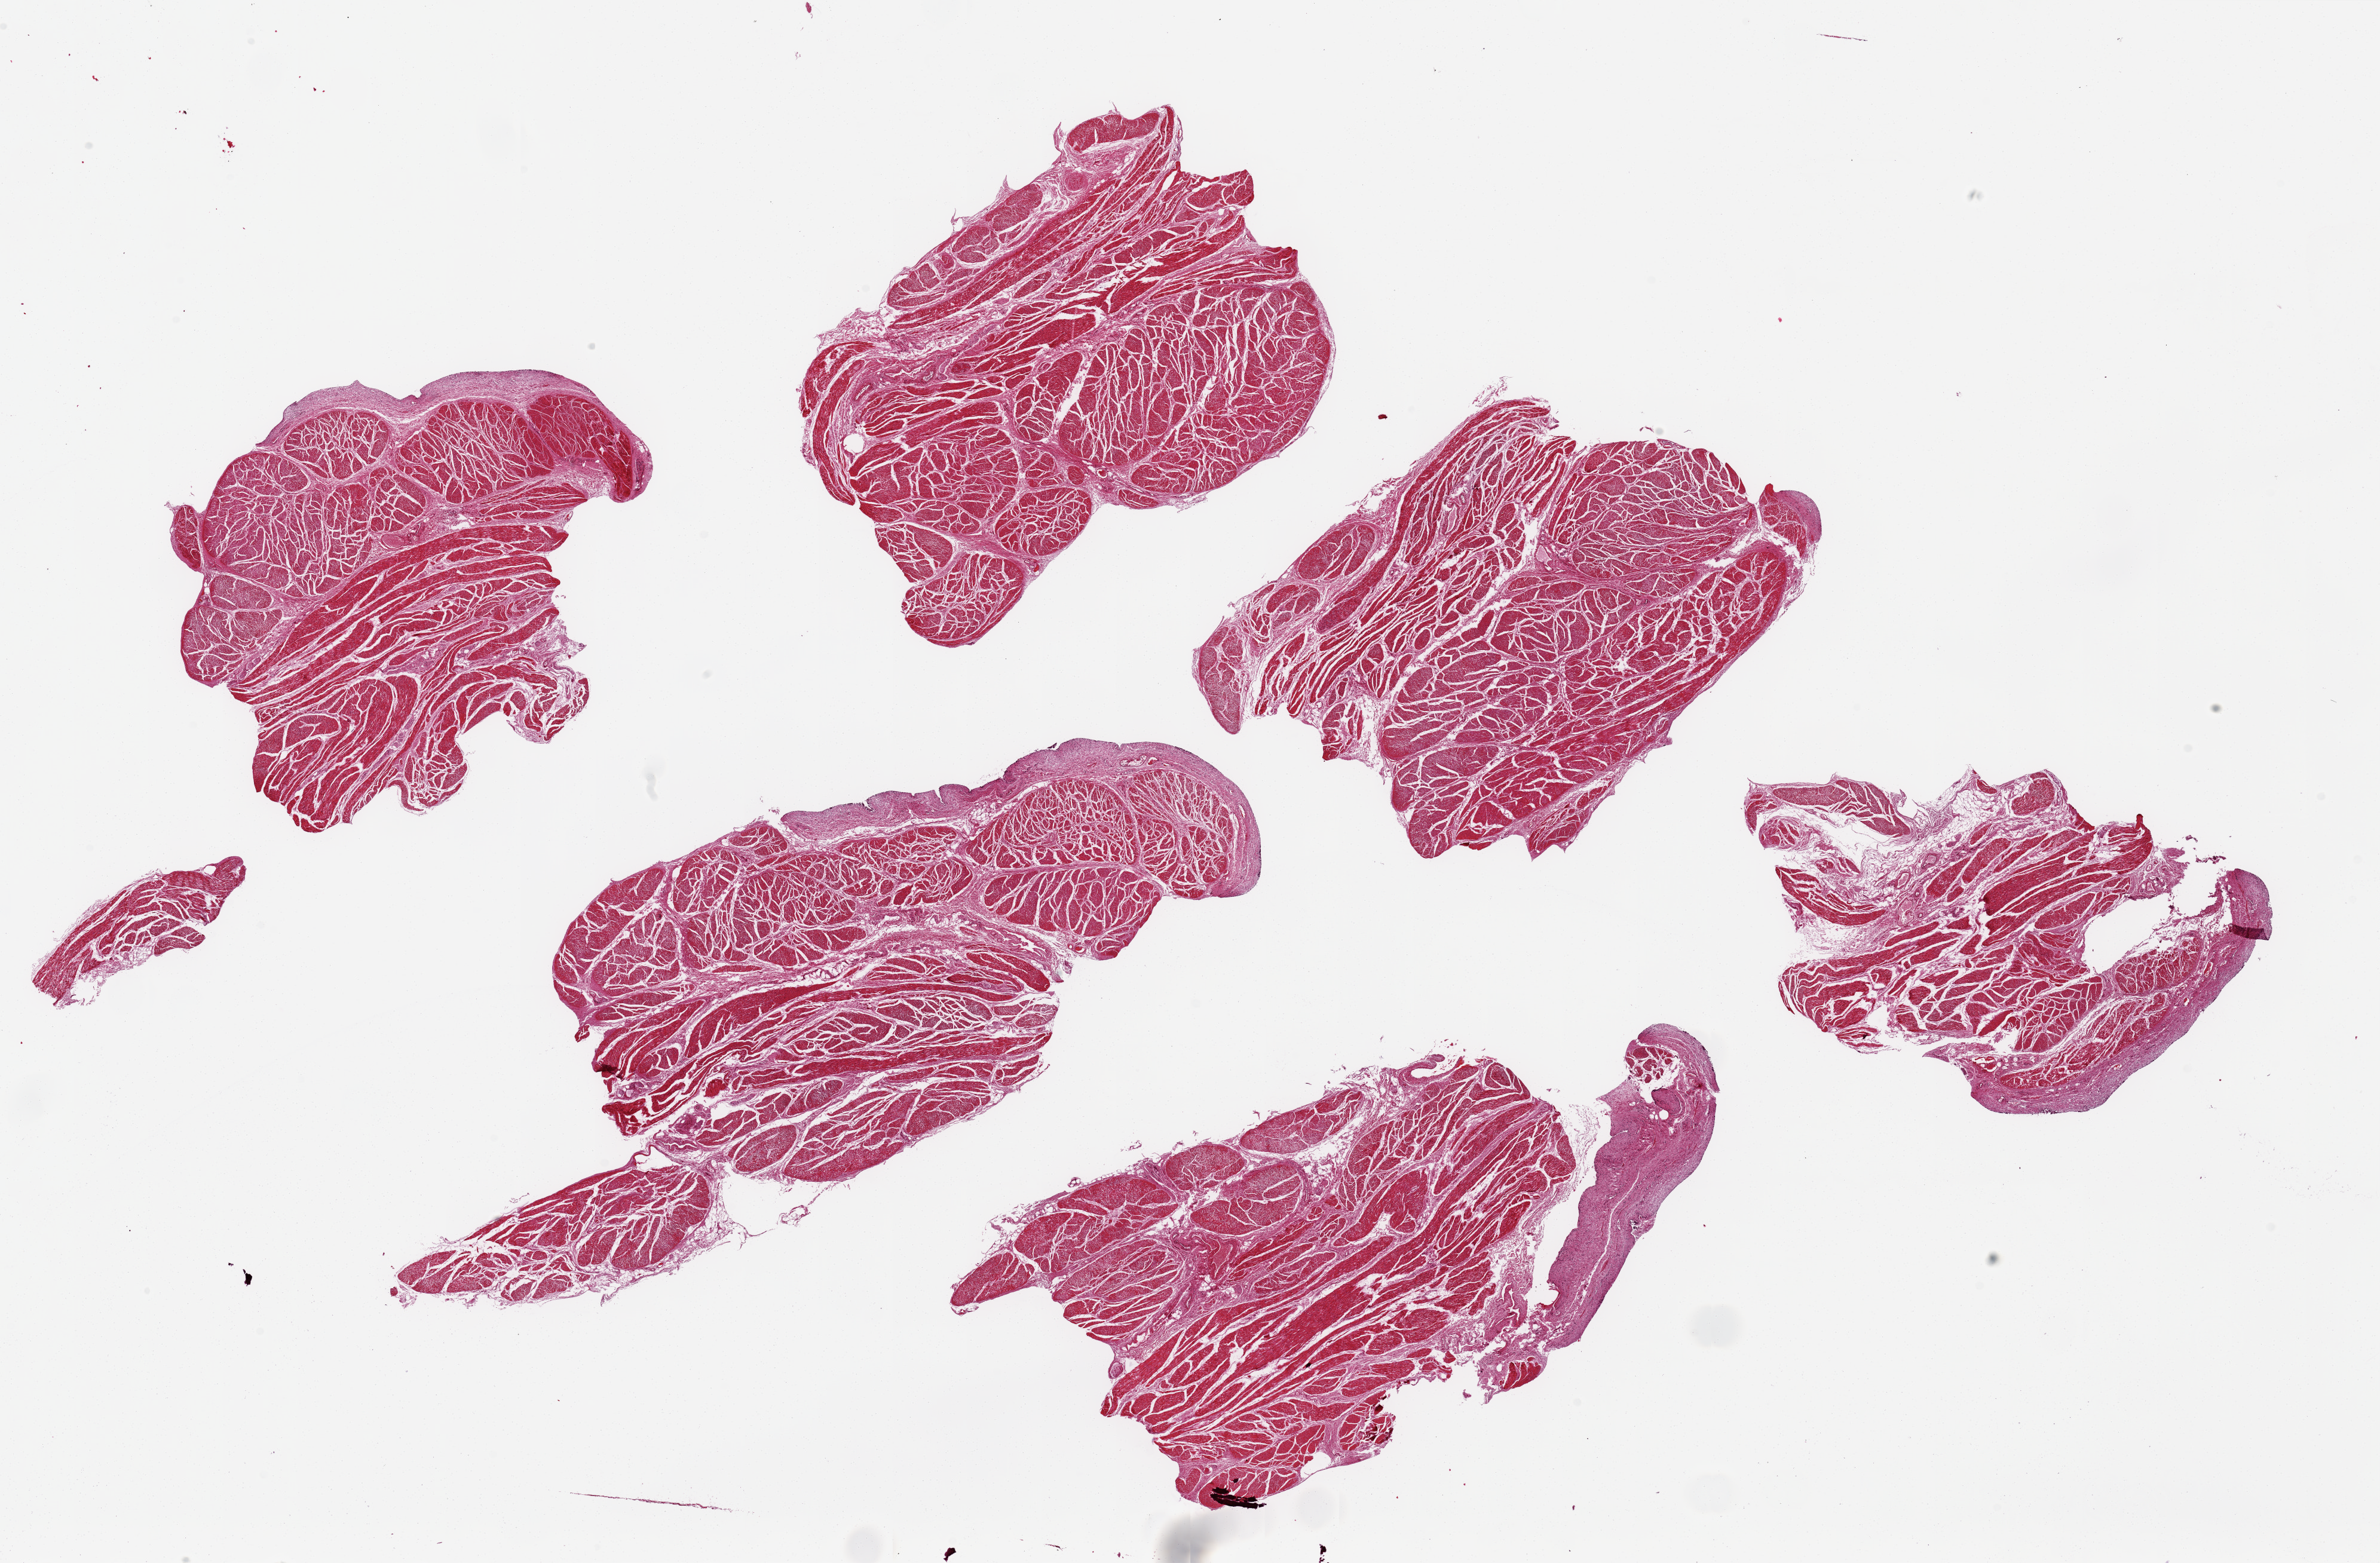
Digitized hematoxylin and eosin (H&E)-stained section, low-resolution overview of the scanned area, about 31.5 x 20.7 mm (acquisition: 20x scan), PAXgene-fixed paraffin-embedded (PFPE) section, section of urinary bladder (target tissue), donor tissue sample. Male donor.
Review note (as recorded): 6 pieces ~6x4mm. All detrusor muscle: Urothelium completely autolyzed/sloughed.